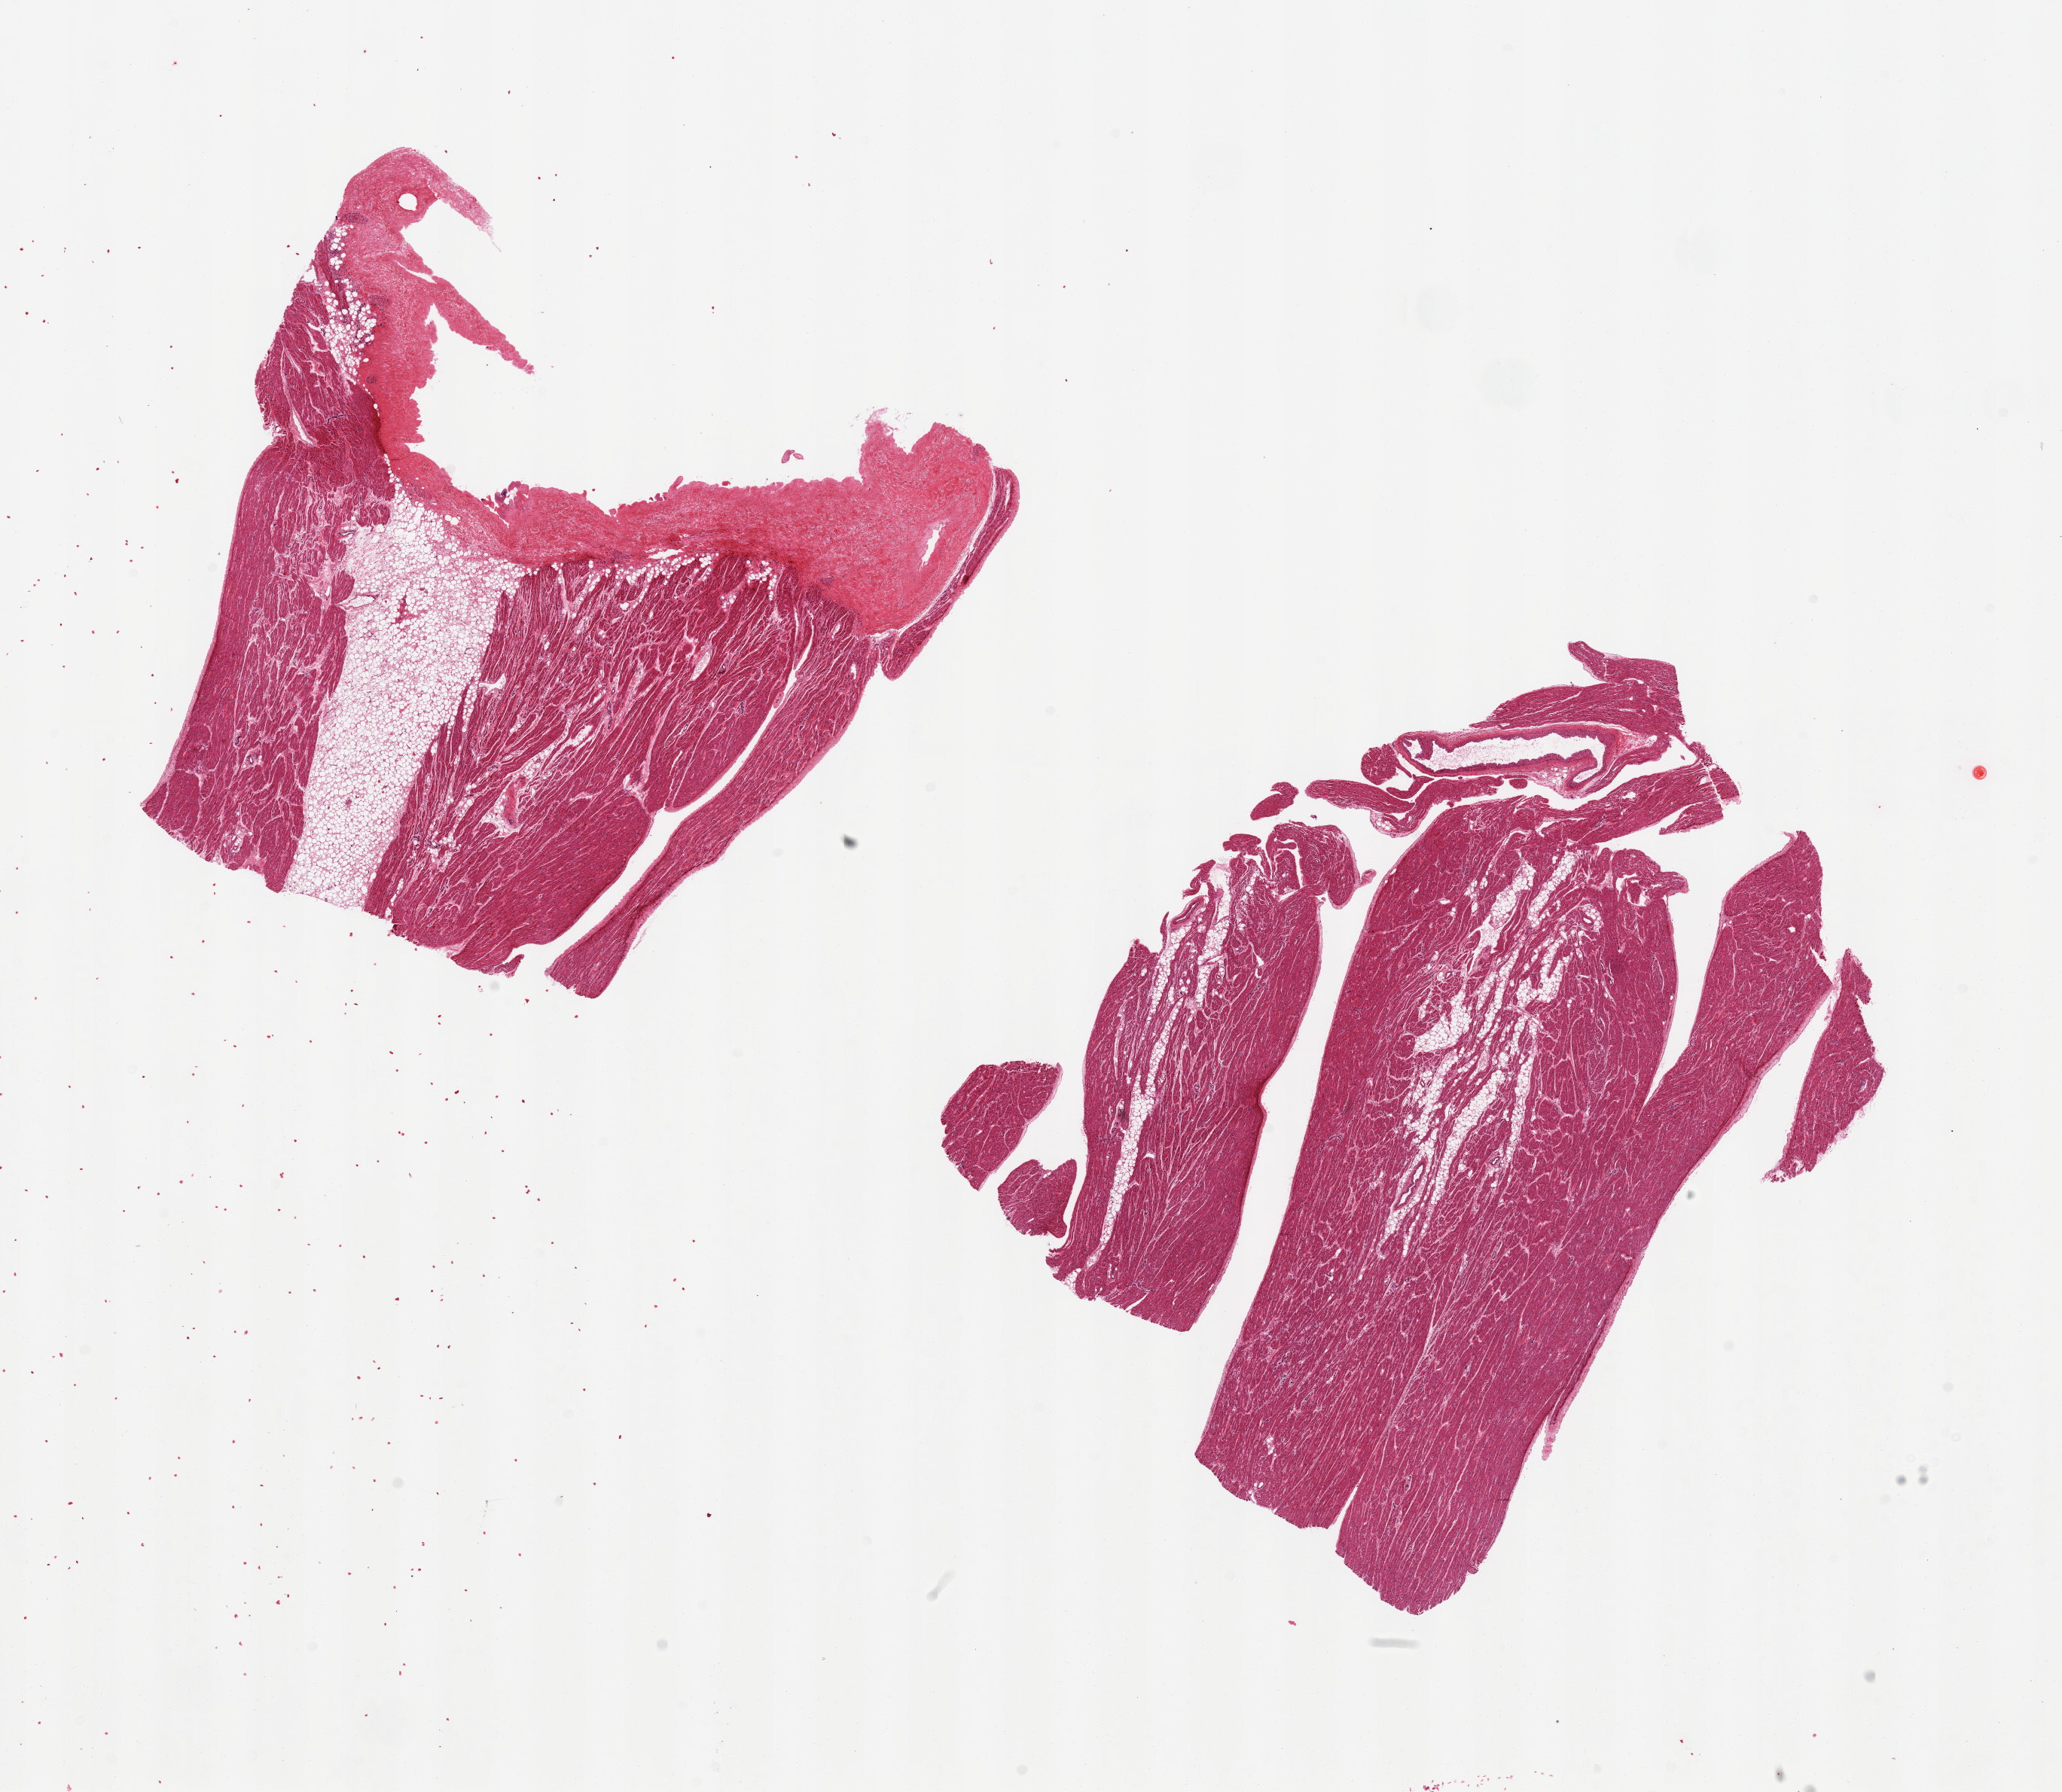
Haematoxylin and eosin whole-slide image — shown as a low-resolution overview of the whole scanned area (about 21.7 x 18.8 mm), PAXgene-fixed, paraffin-embedded tissue, target tissue: auricular appendage, donor tissue sample. Female donor.
Review note (as recorded): 2 pieces, one piece is 10% fat/10% fibrous.